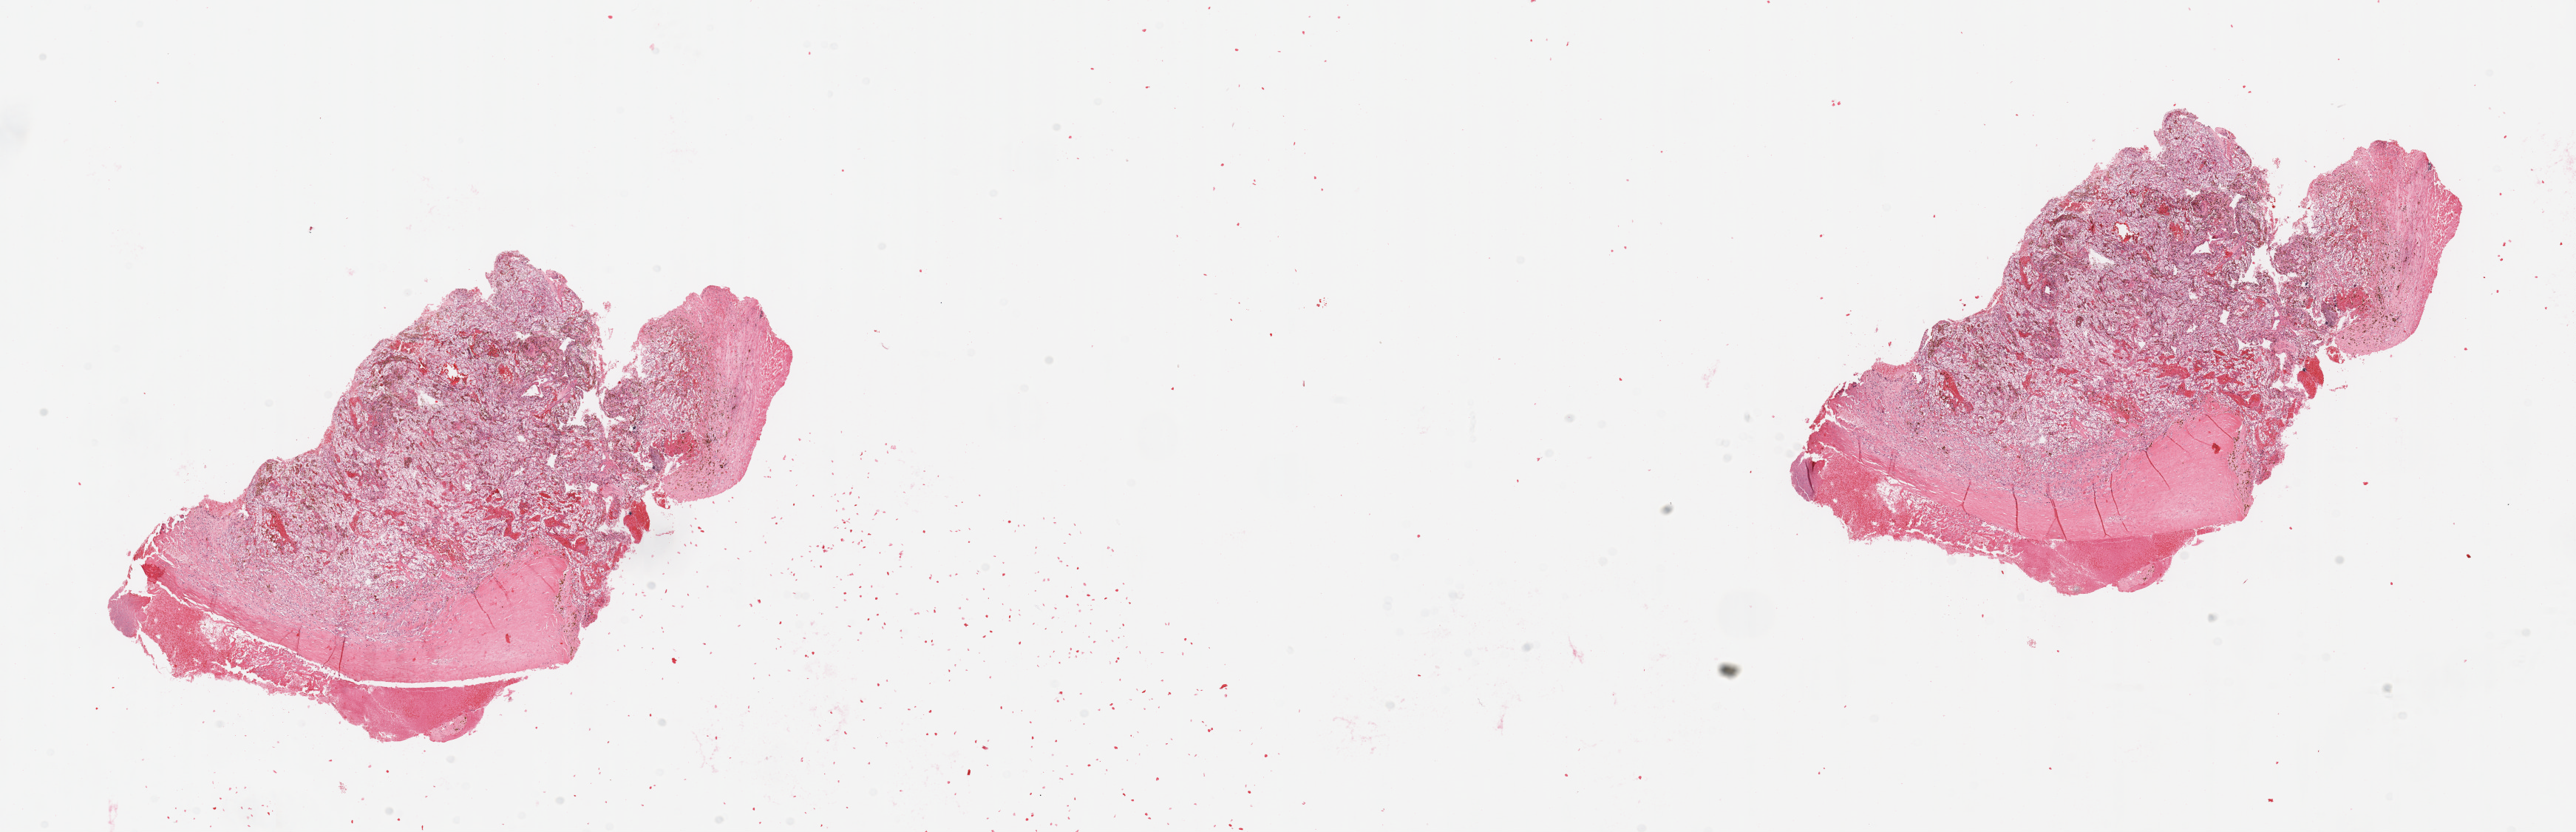
Whole-slide histology image, Hematoxylin and eosin (H&E) stained — a low-resolution overview of the entire scanned area, about 27.6 x 8.9 mm (acquisition: 20x scan), tumour tissue sample, sampled site: kidney. Patient: female, age 51 years. Histologic grade: G3 (poorly differentiated). Composition of this section per pathologist review: tumour nuclei 80%, necrosis 5%.
Histologic diagnosis: Renal cell carcinoma, NOS. AJCC pathologic stage: IV.